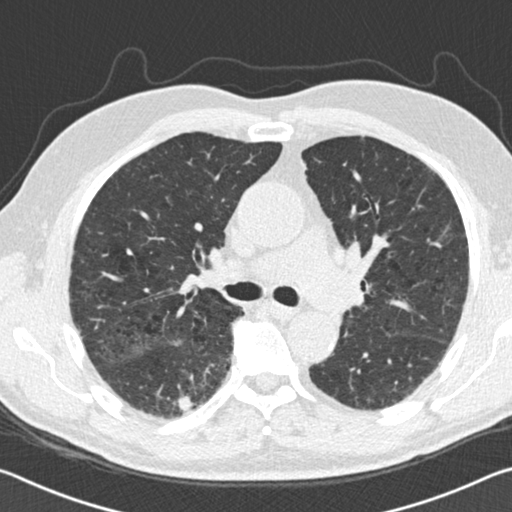
Low-dose screening chest CT, one axial slice; position 85 of 142 along the scan axis; reconstruction kernel B30f; lung window (W 1500 / L -600 HU); 2 mm slice thickness; 512 × 512 image matrix, field of view 340 × 340 mm.
Outlined on this slice (outlined manually by an expert reader):
- lesion 1 (tumor, lower lobe of right lung): bounding box <173,394,197,413> (left, top, right, bottom; pixels)